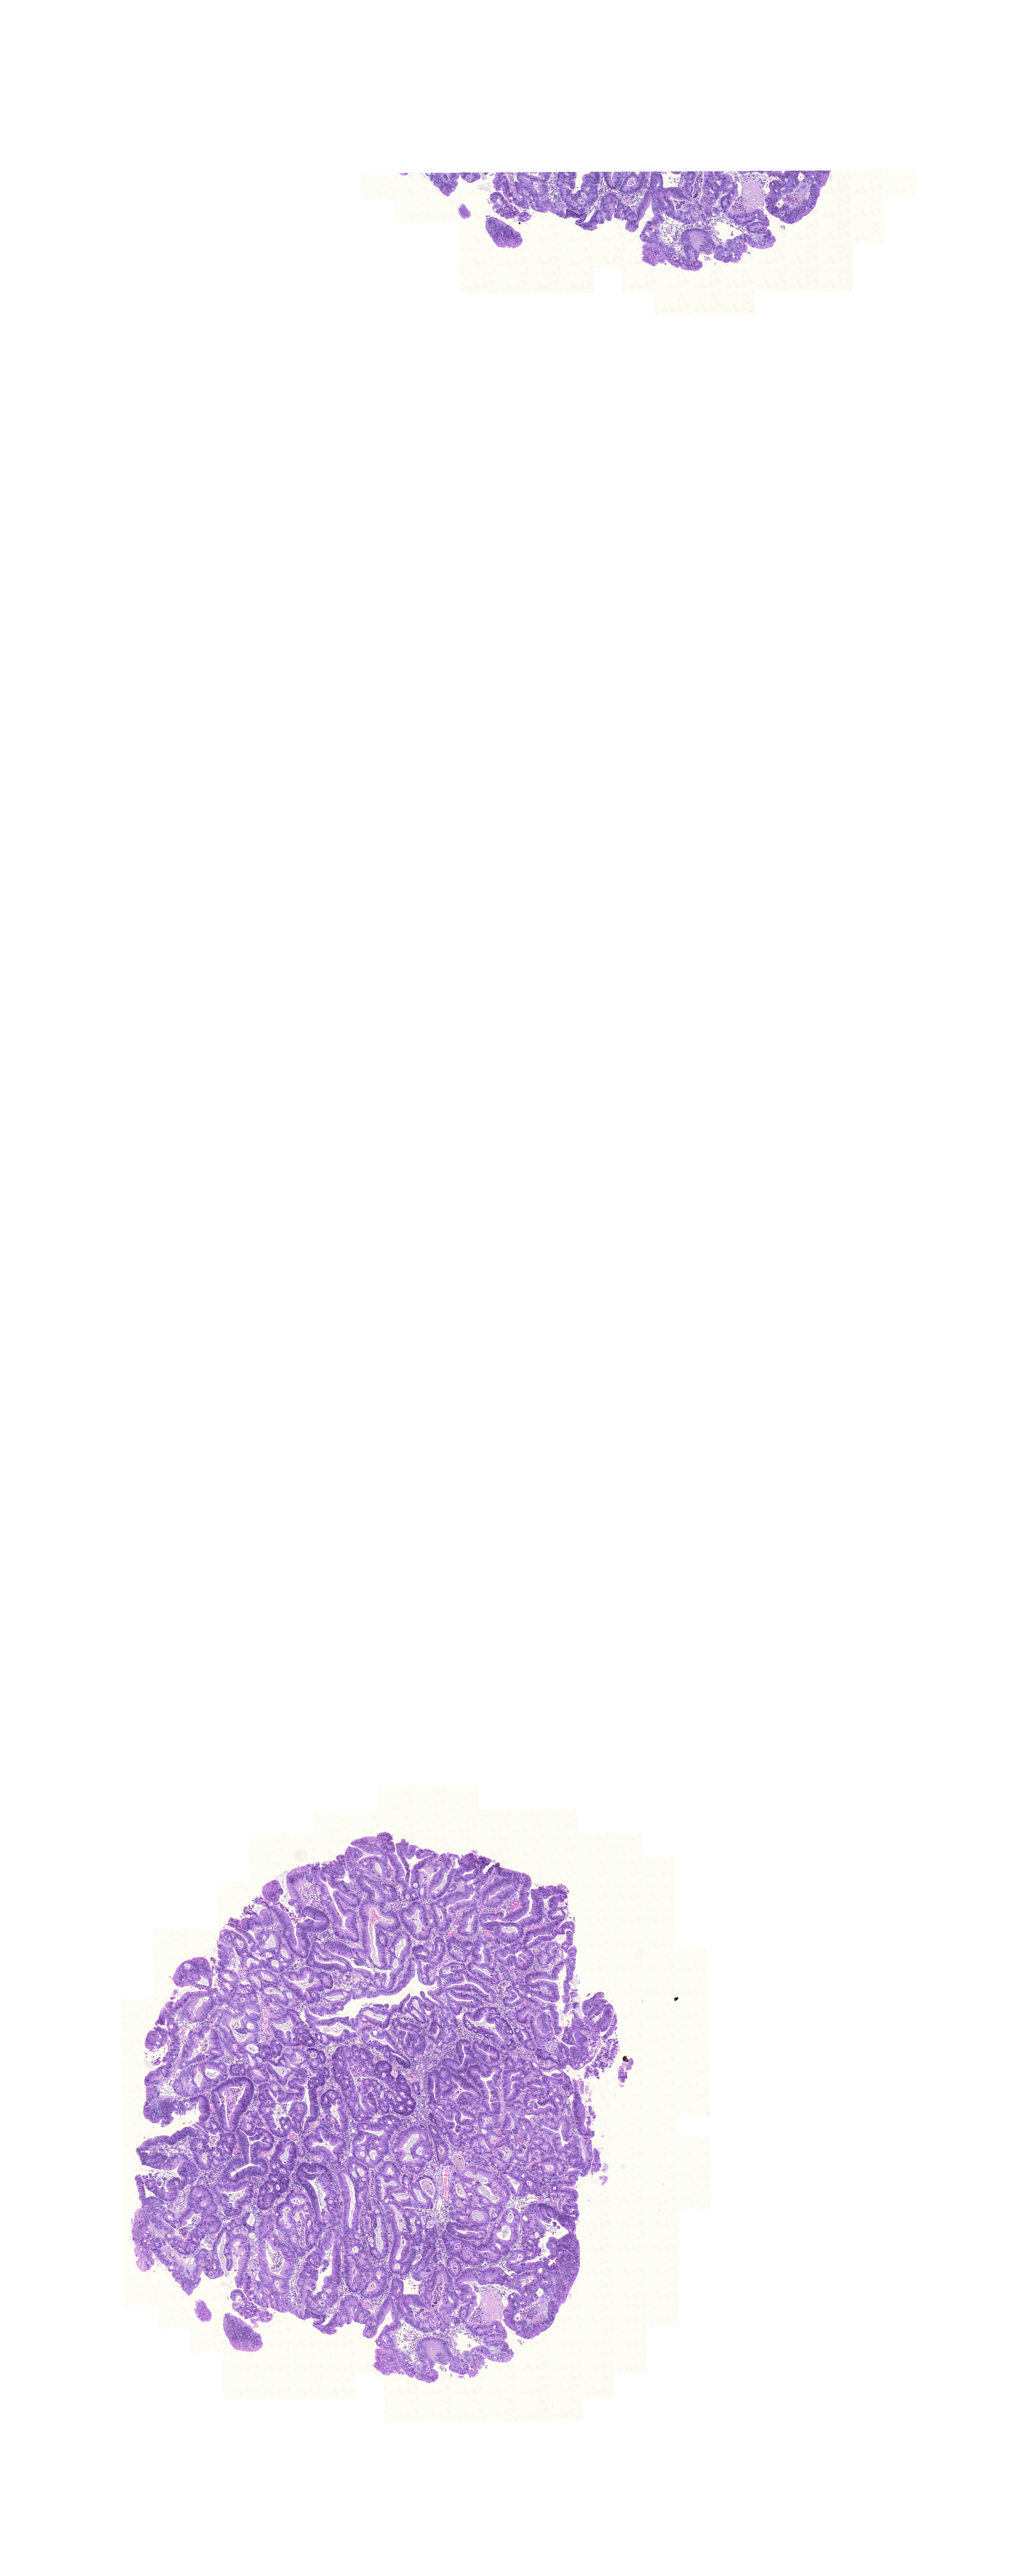
Digitized H&E-stained tissue section (whole slide), a low-resolution overview of the entire scanned area, about 9.1 x 22.8 mm (from a 20x scan); formalin-fixed paraffin-embedded (FFPE) diagnostic section; sample: primary tumour, rectum. Male, age 58 years at initial diagnosis.
• AJCC pathologic stage: IIIB
• pathologic diagnosis: Adenocarcinoma, NOS
• TNM: T3 N1 M0